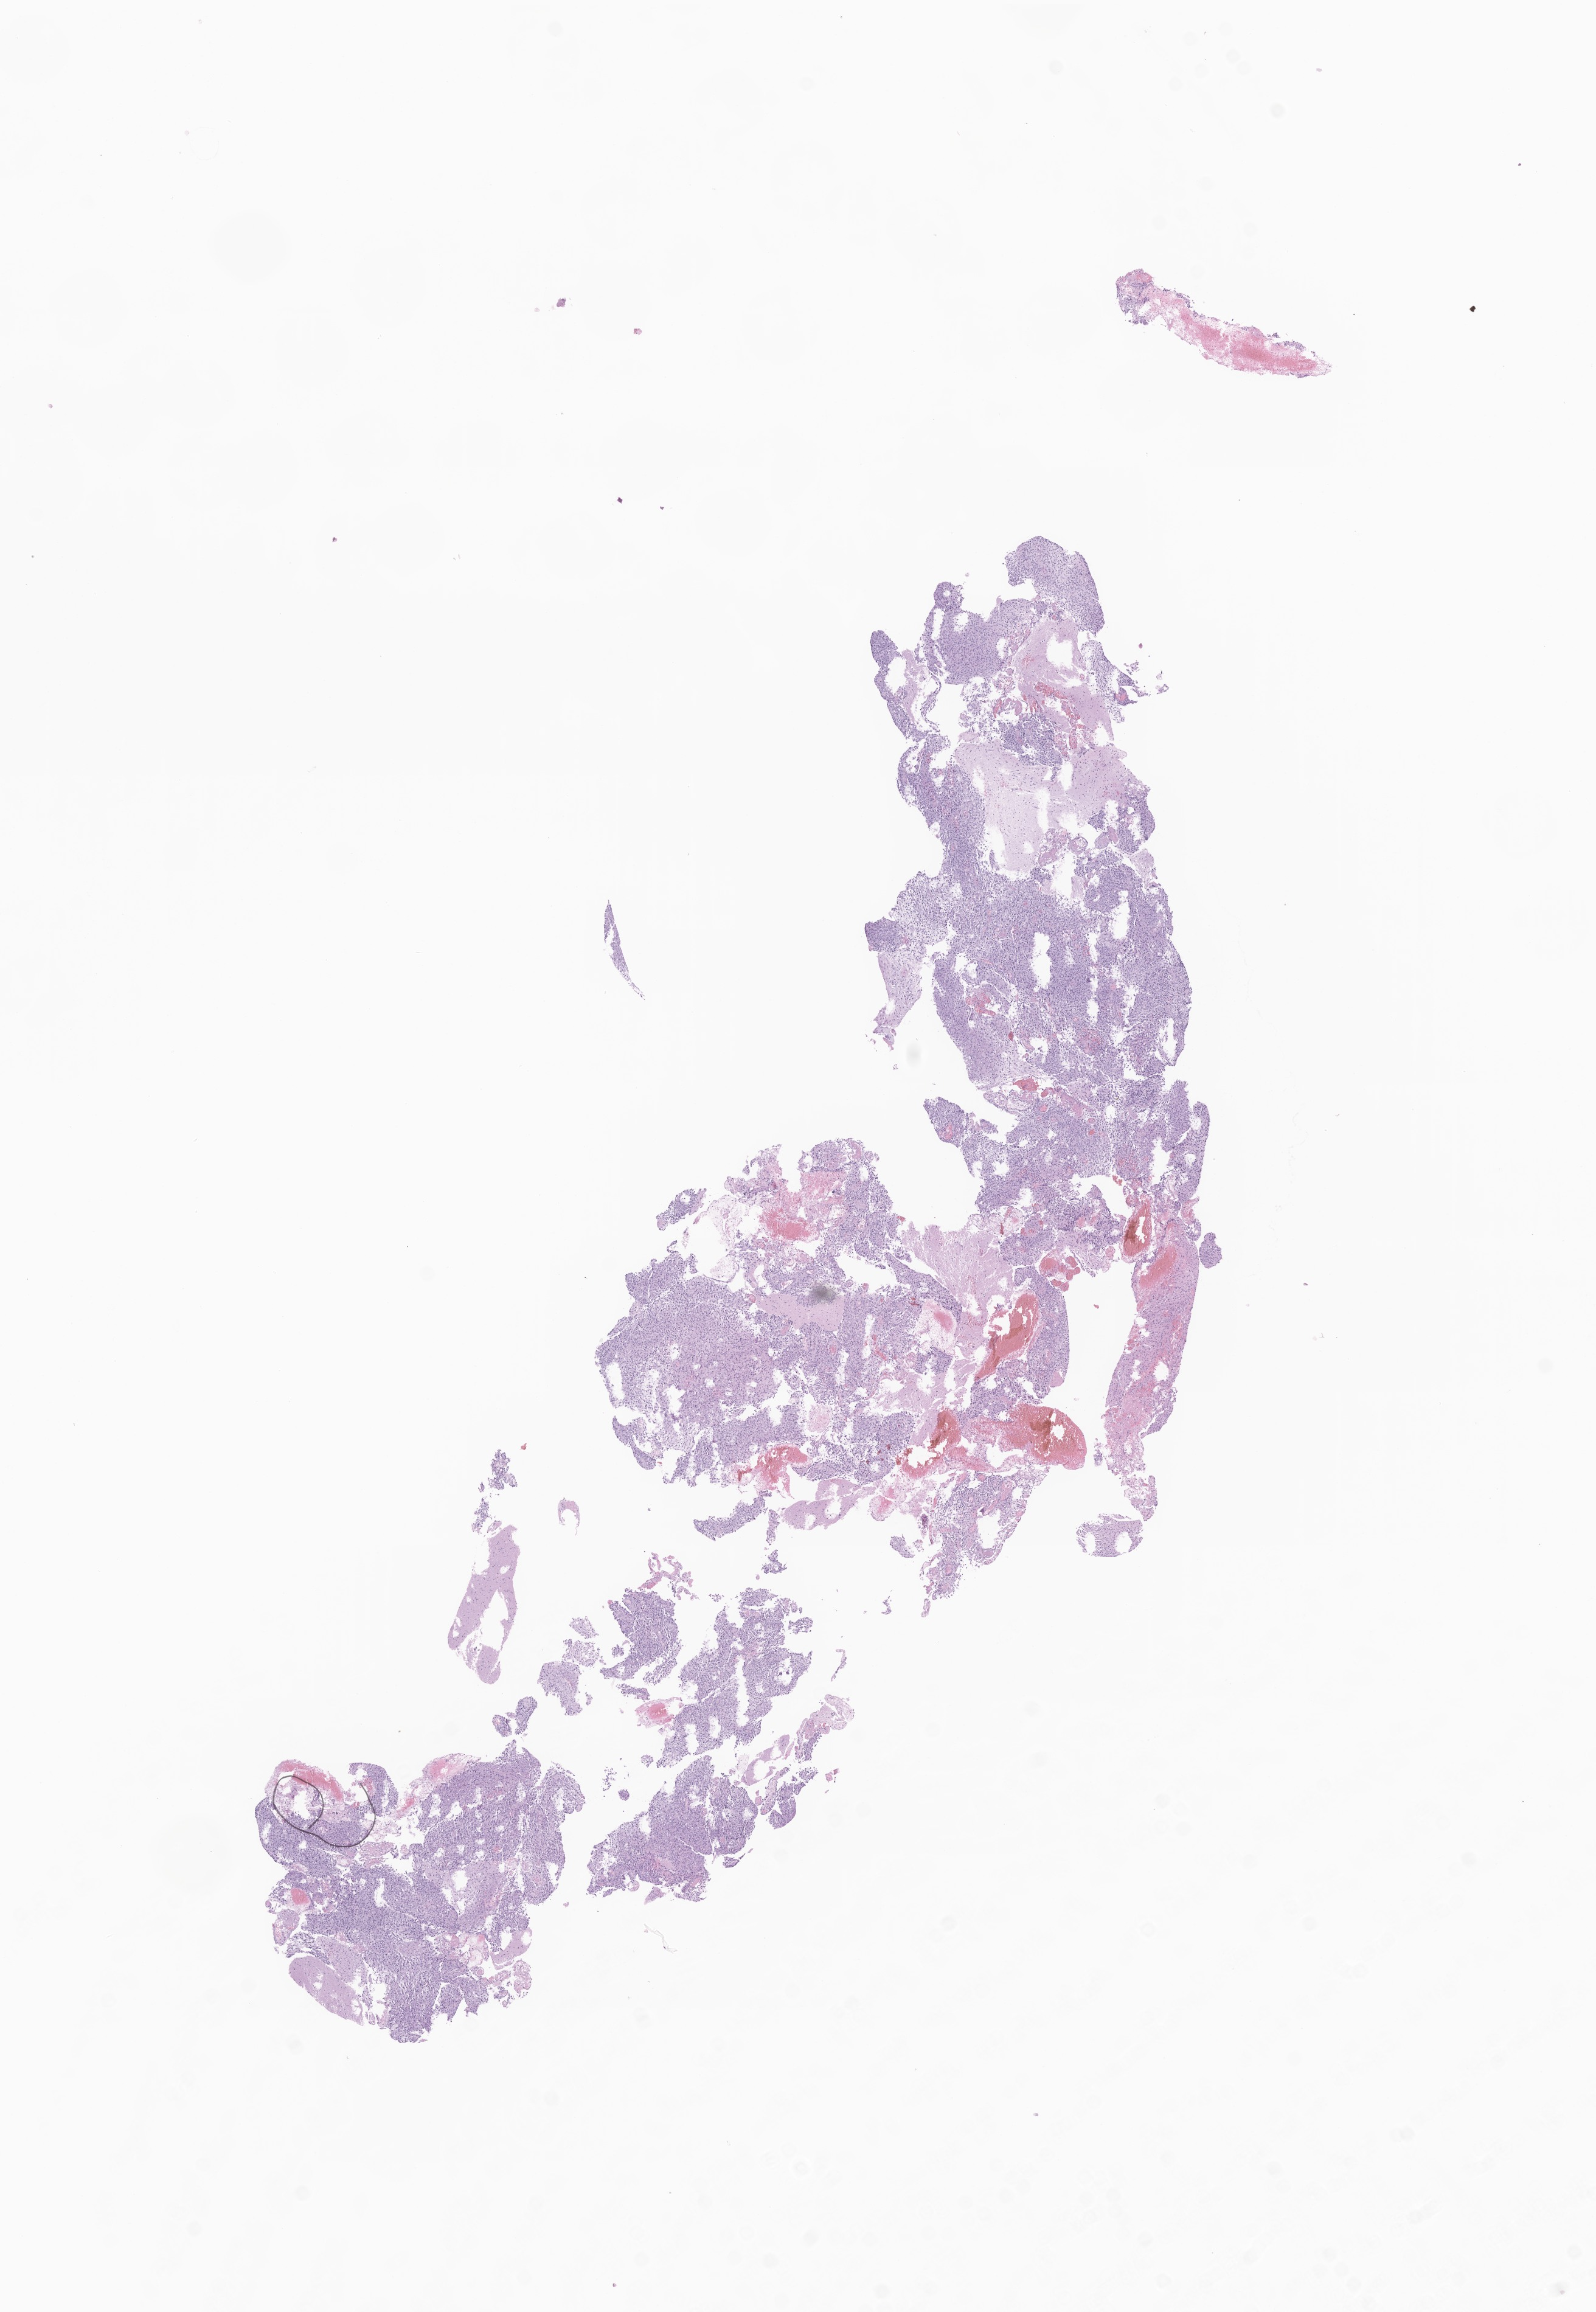
Whole-slide image, H&E stain of tumor tissue from the brain, whole scanned area (about 11.1 x 16.0 mm) shown as a low-resolution overview; formalin-fixed paraffin-embedded section. Female patient, age 129 months (10 years 9 months).
Diagnosis (ICD-O-3 morphology term): Glioma, malignant.